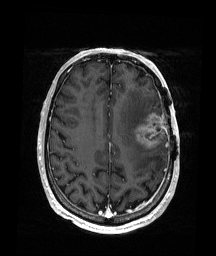
Brain MRI from a brain-tumour surgery series, one axial slice. Position 66 of 176 along the scan axis. T1-weighted post-contrast. 1 mm slice thickness. 216 × 256 image matrix. From the clinical record (not read from this slice): histopathology: Glioblastoma; WHO grade: 4; IDH mutation: no; tumour location: Left Frontal.
Structures marked on this image (outlined manually by an expert reader):
- tumour: box from (x=134, y=112) to (x=167, y=148) px